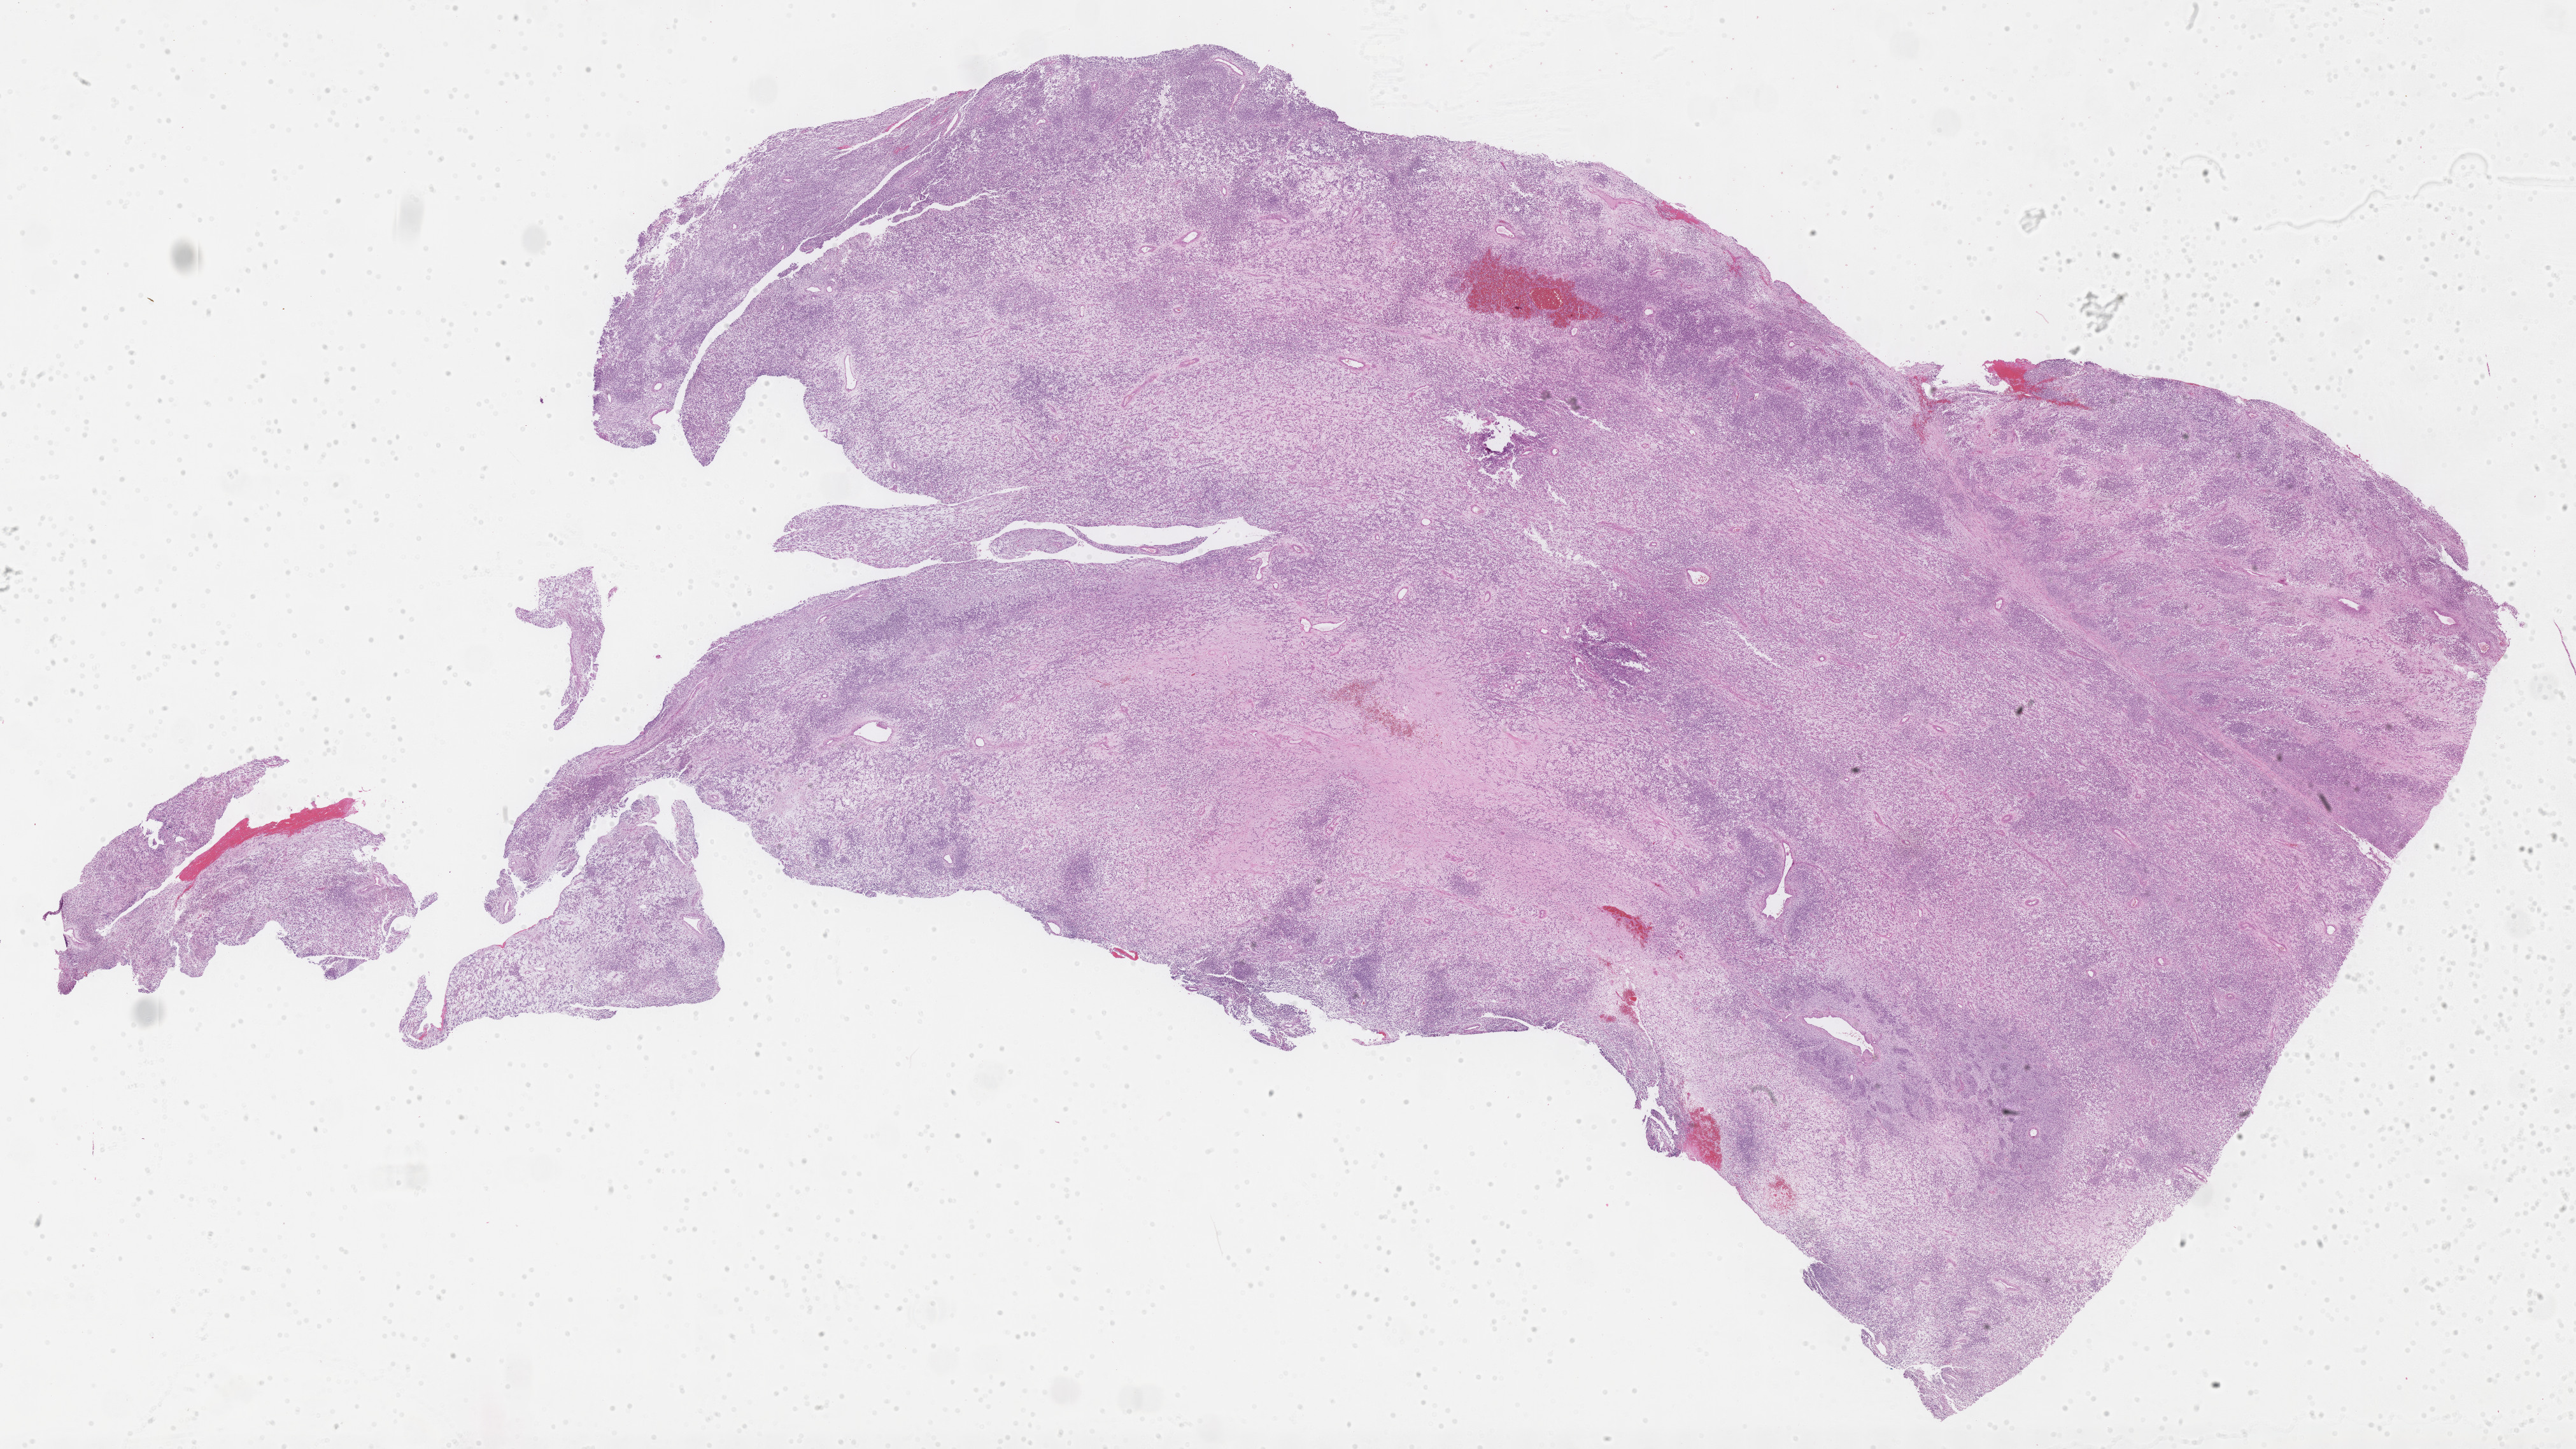
Hematoxylin and eosin (H&E) whole-slide image of tumor tissue — a low-resolution overview of the entire scanned area, about 32.7 x 18.4 mm. FFPE section. Sample anatomic site: soft tissue, abdomen-right. Patient: male, age 3.8 years at diagnosis.
Diagnosis: rhabdomyosarcoma; histological classification: embryonal rhabdomyosarcoma.